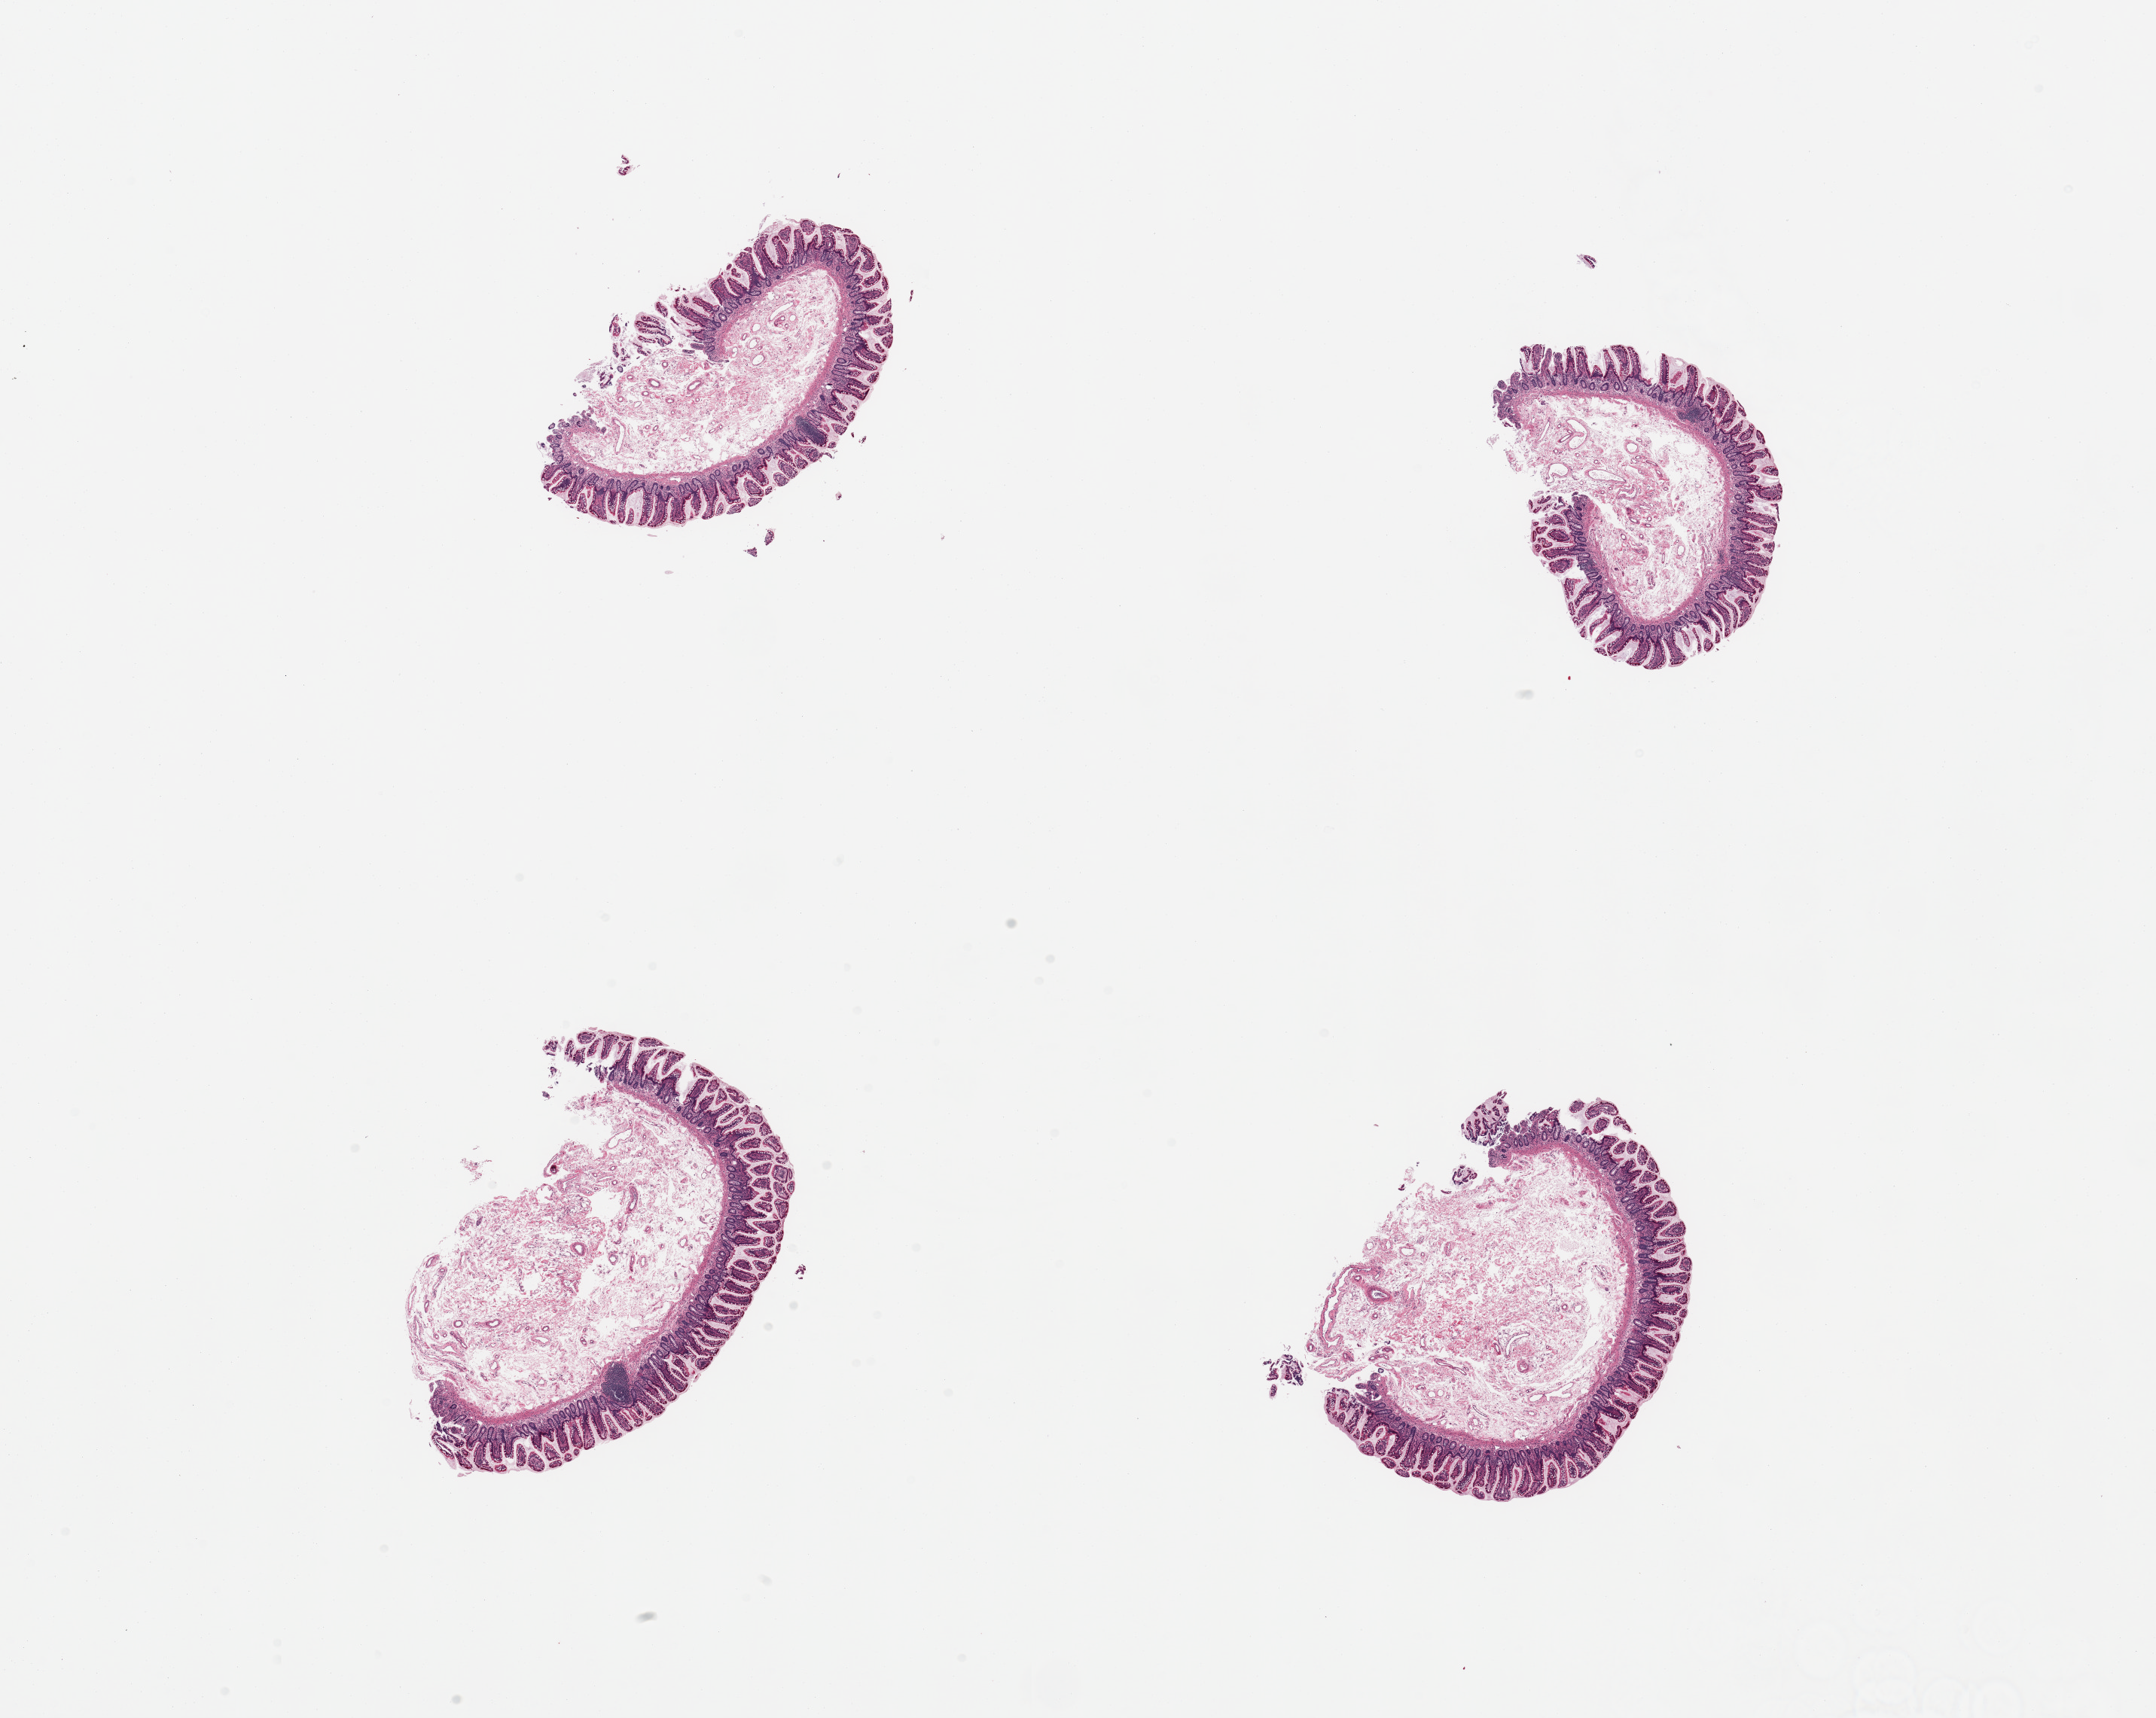
Digitized H&E-stained section, shown as a low-resolution overview of the whole scanned area (about 22.6 x 18.0 mm, from a 20x scan). Male donor.
• specimen: PAXgene-fixed paraffin-embedded (PFPE) section; section of ileum (target tissue); donor tissue sample